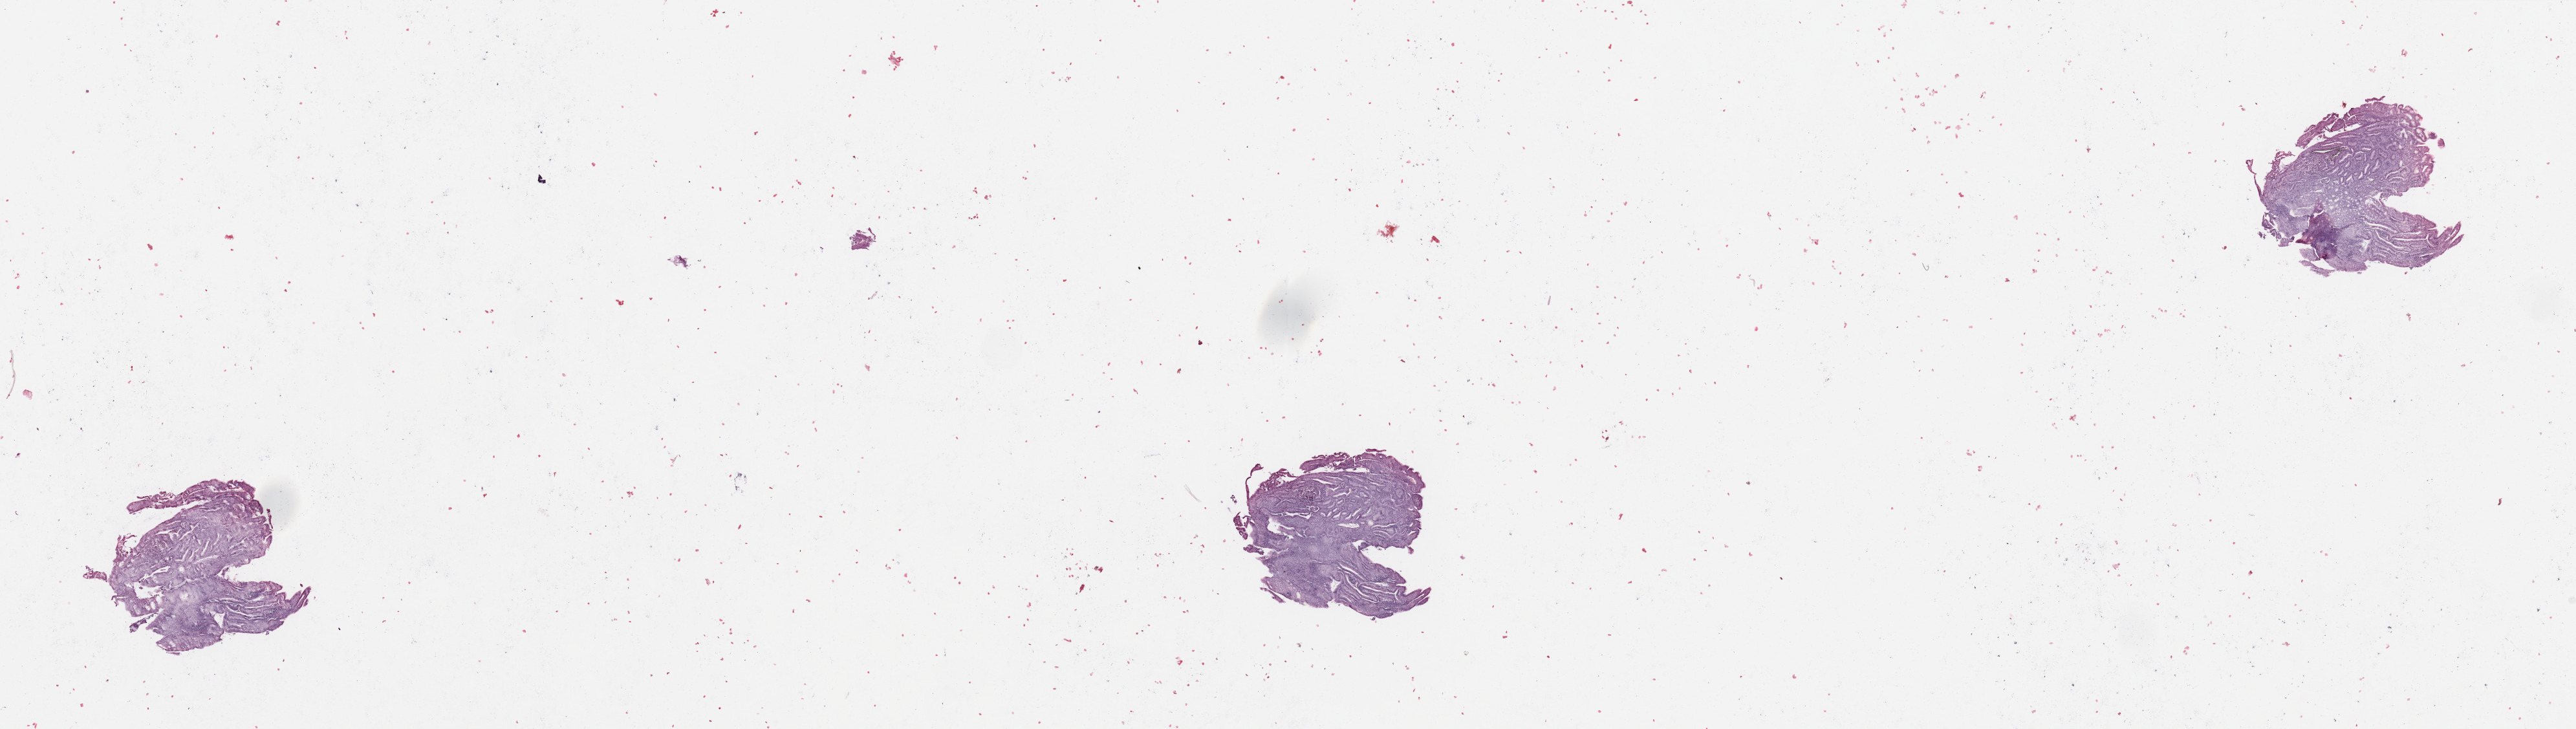
Whole-slide histology image, H&E-stained — shown as a low-resolution overview of the whole scanned area (about 31.5 x 8.9 mm, acquisition: 20x scan); tumour tissue sample, sampled site: uterus. Female, 53 y/o. Slide review estimates, as recorded: tumour nuclei 90%, necrosis 2%.
Diagnosis: Endometrioid adenocarcinoma, NOS.